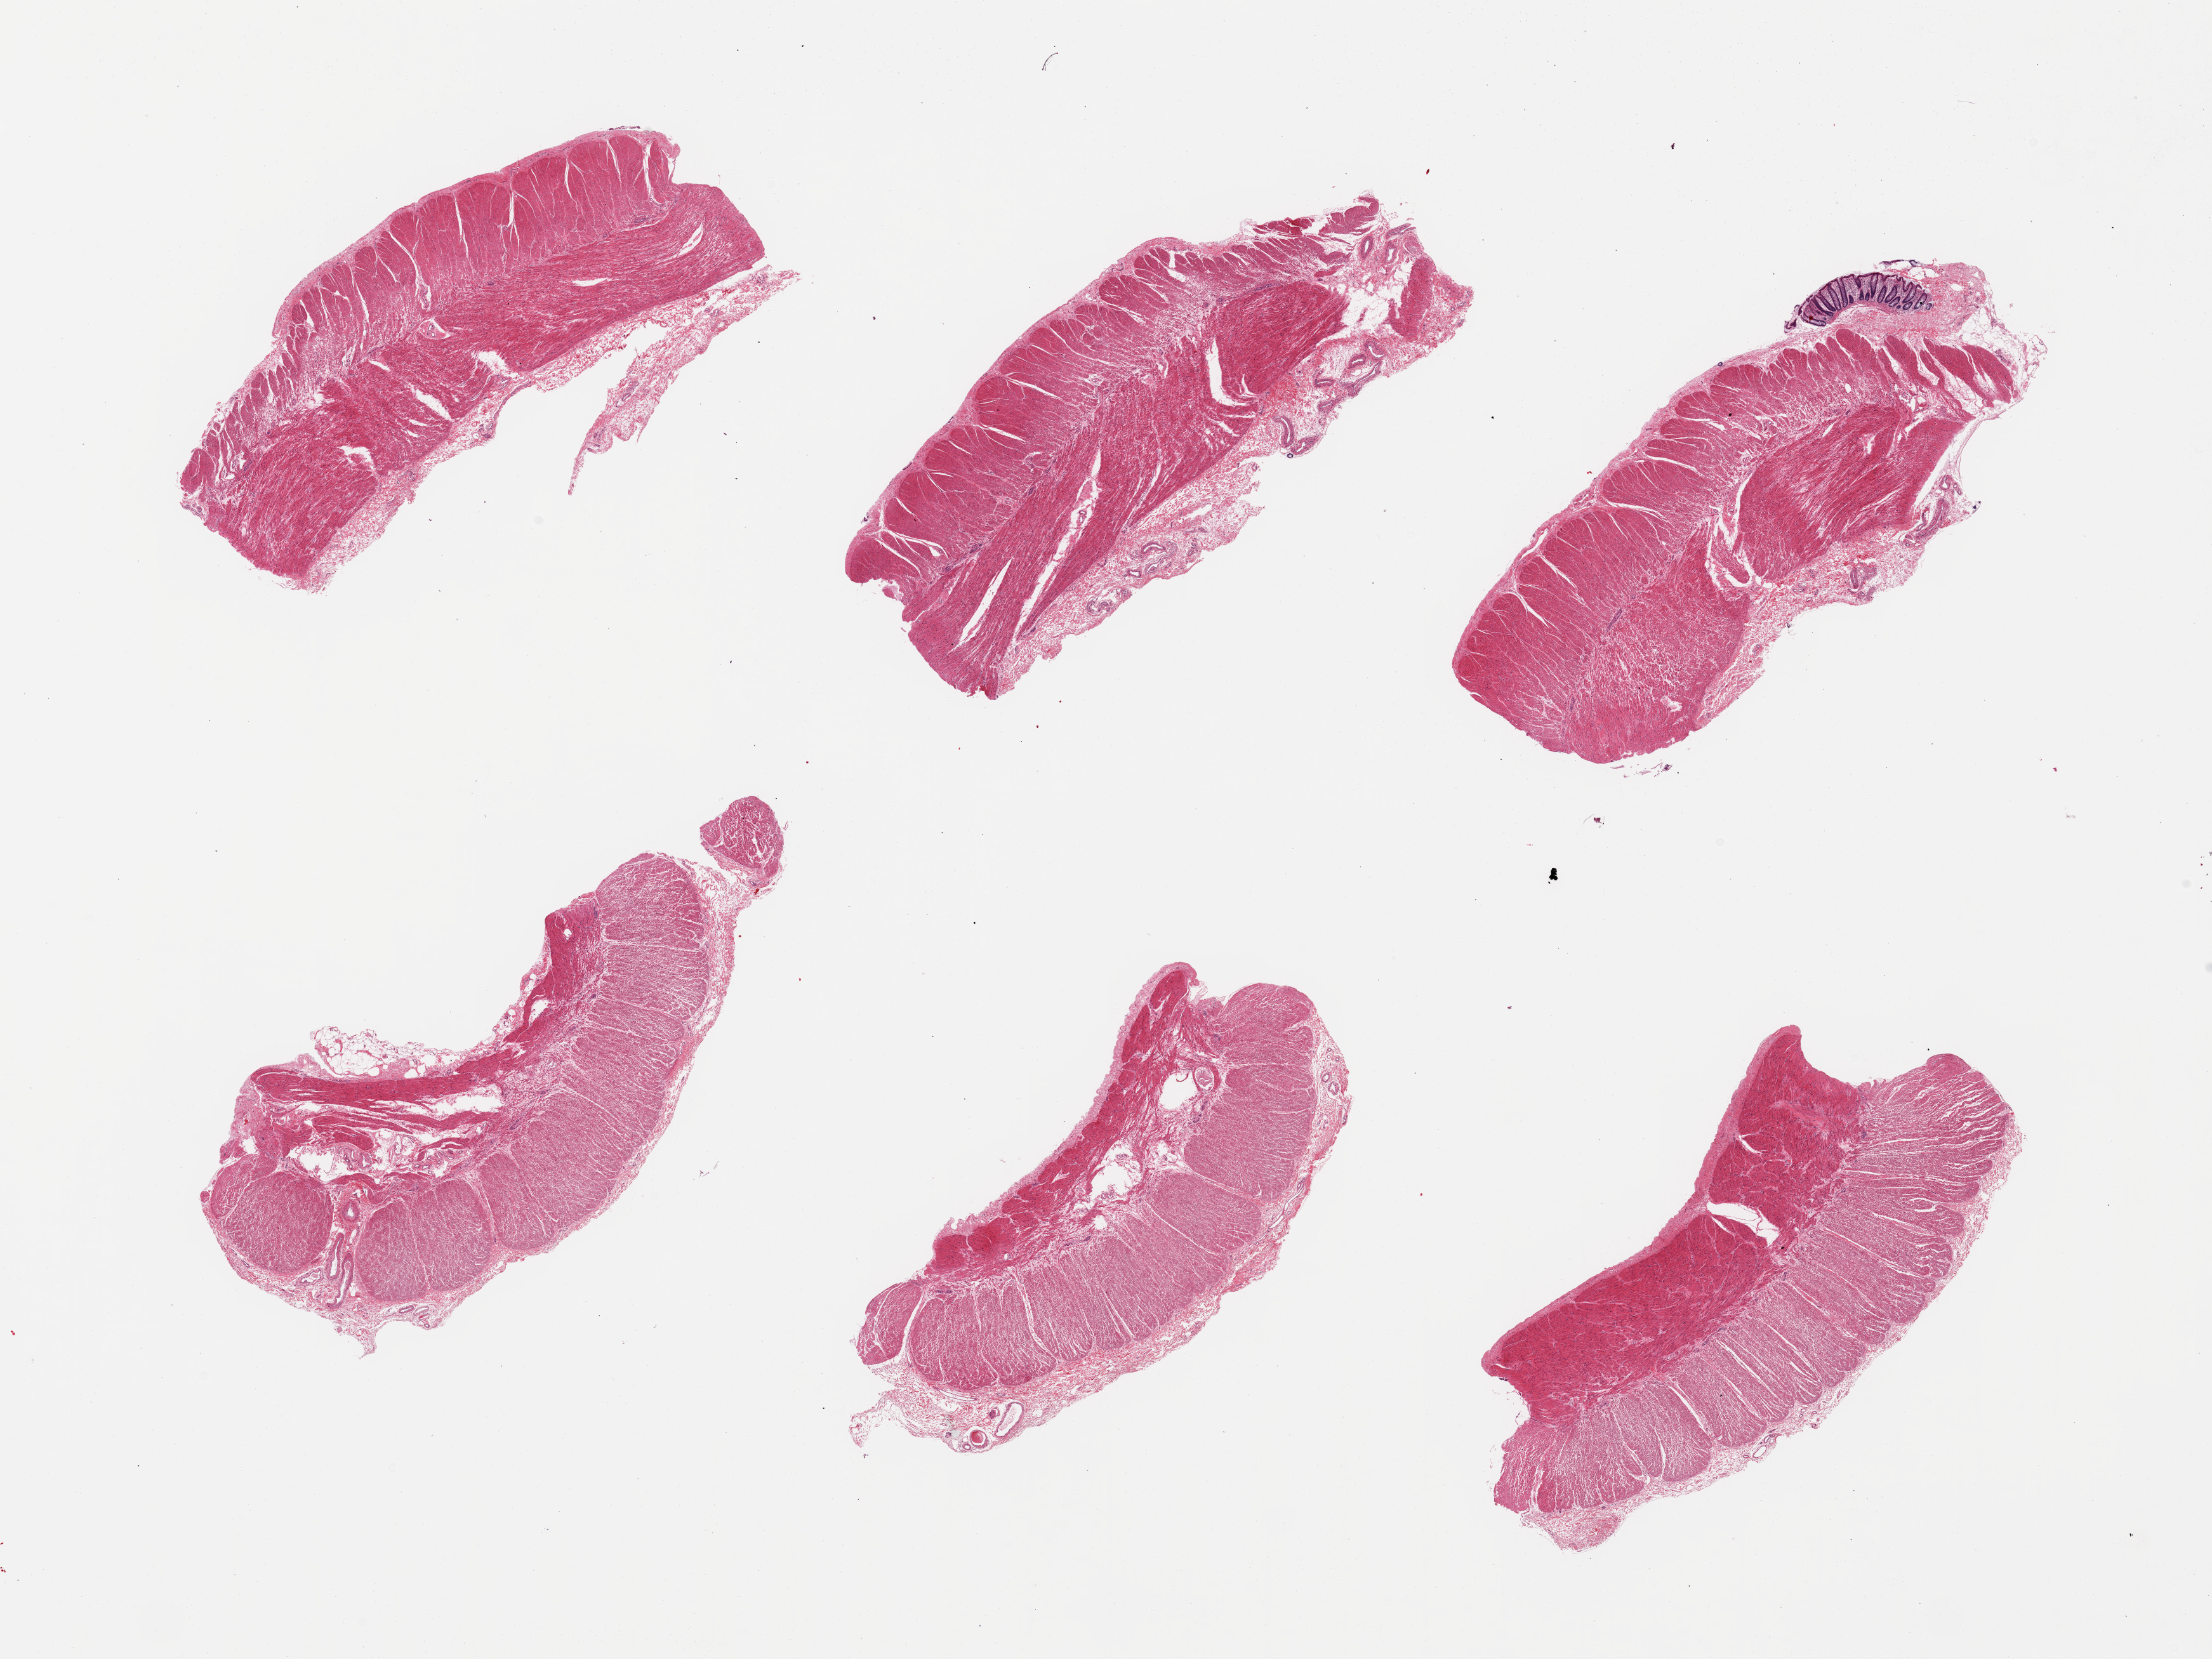
Whole-slide image, haematoxylin and eosin stain — a low-resolution overview of the entire scanned area, about 27.6 x 20.7 mm. PAXgene-fixed, paraffin-embedded tissue. Sampled site (target tissue): sigmoid colon. Tissue donor sample. Donor sex: female.
• reviewer comment on this tissue sample: 6 pieces, all muscularis, trace 'contaminant' mucosa